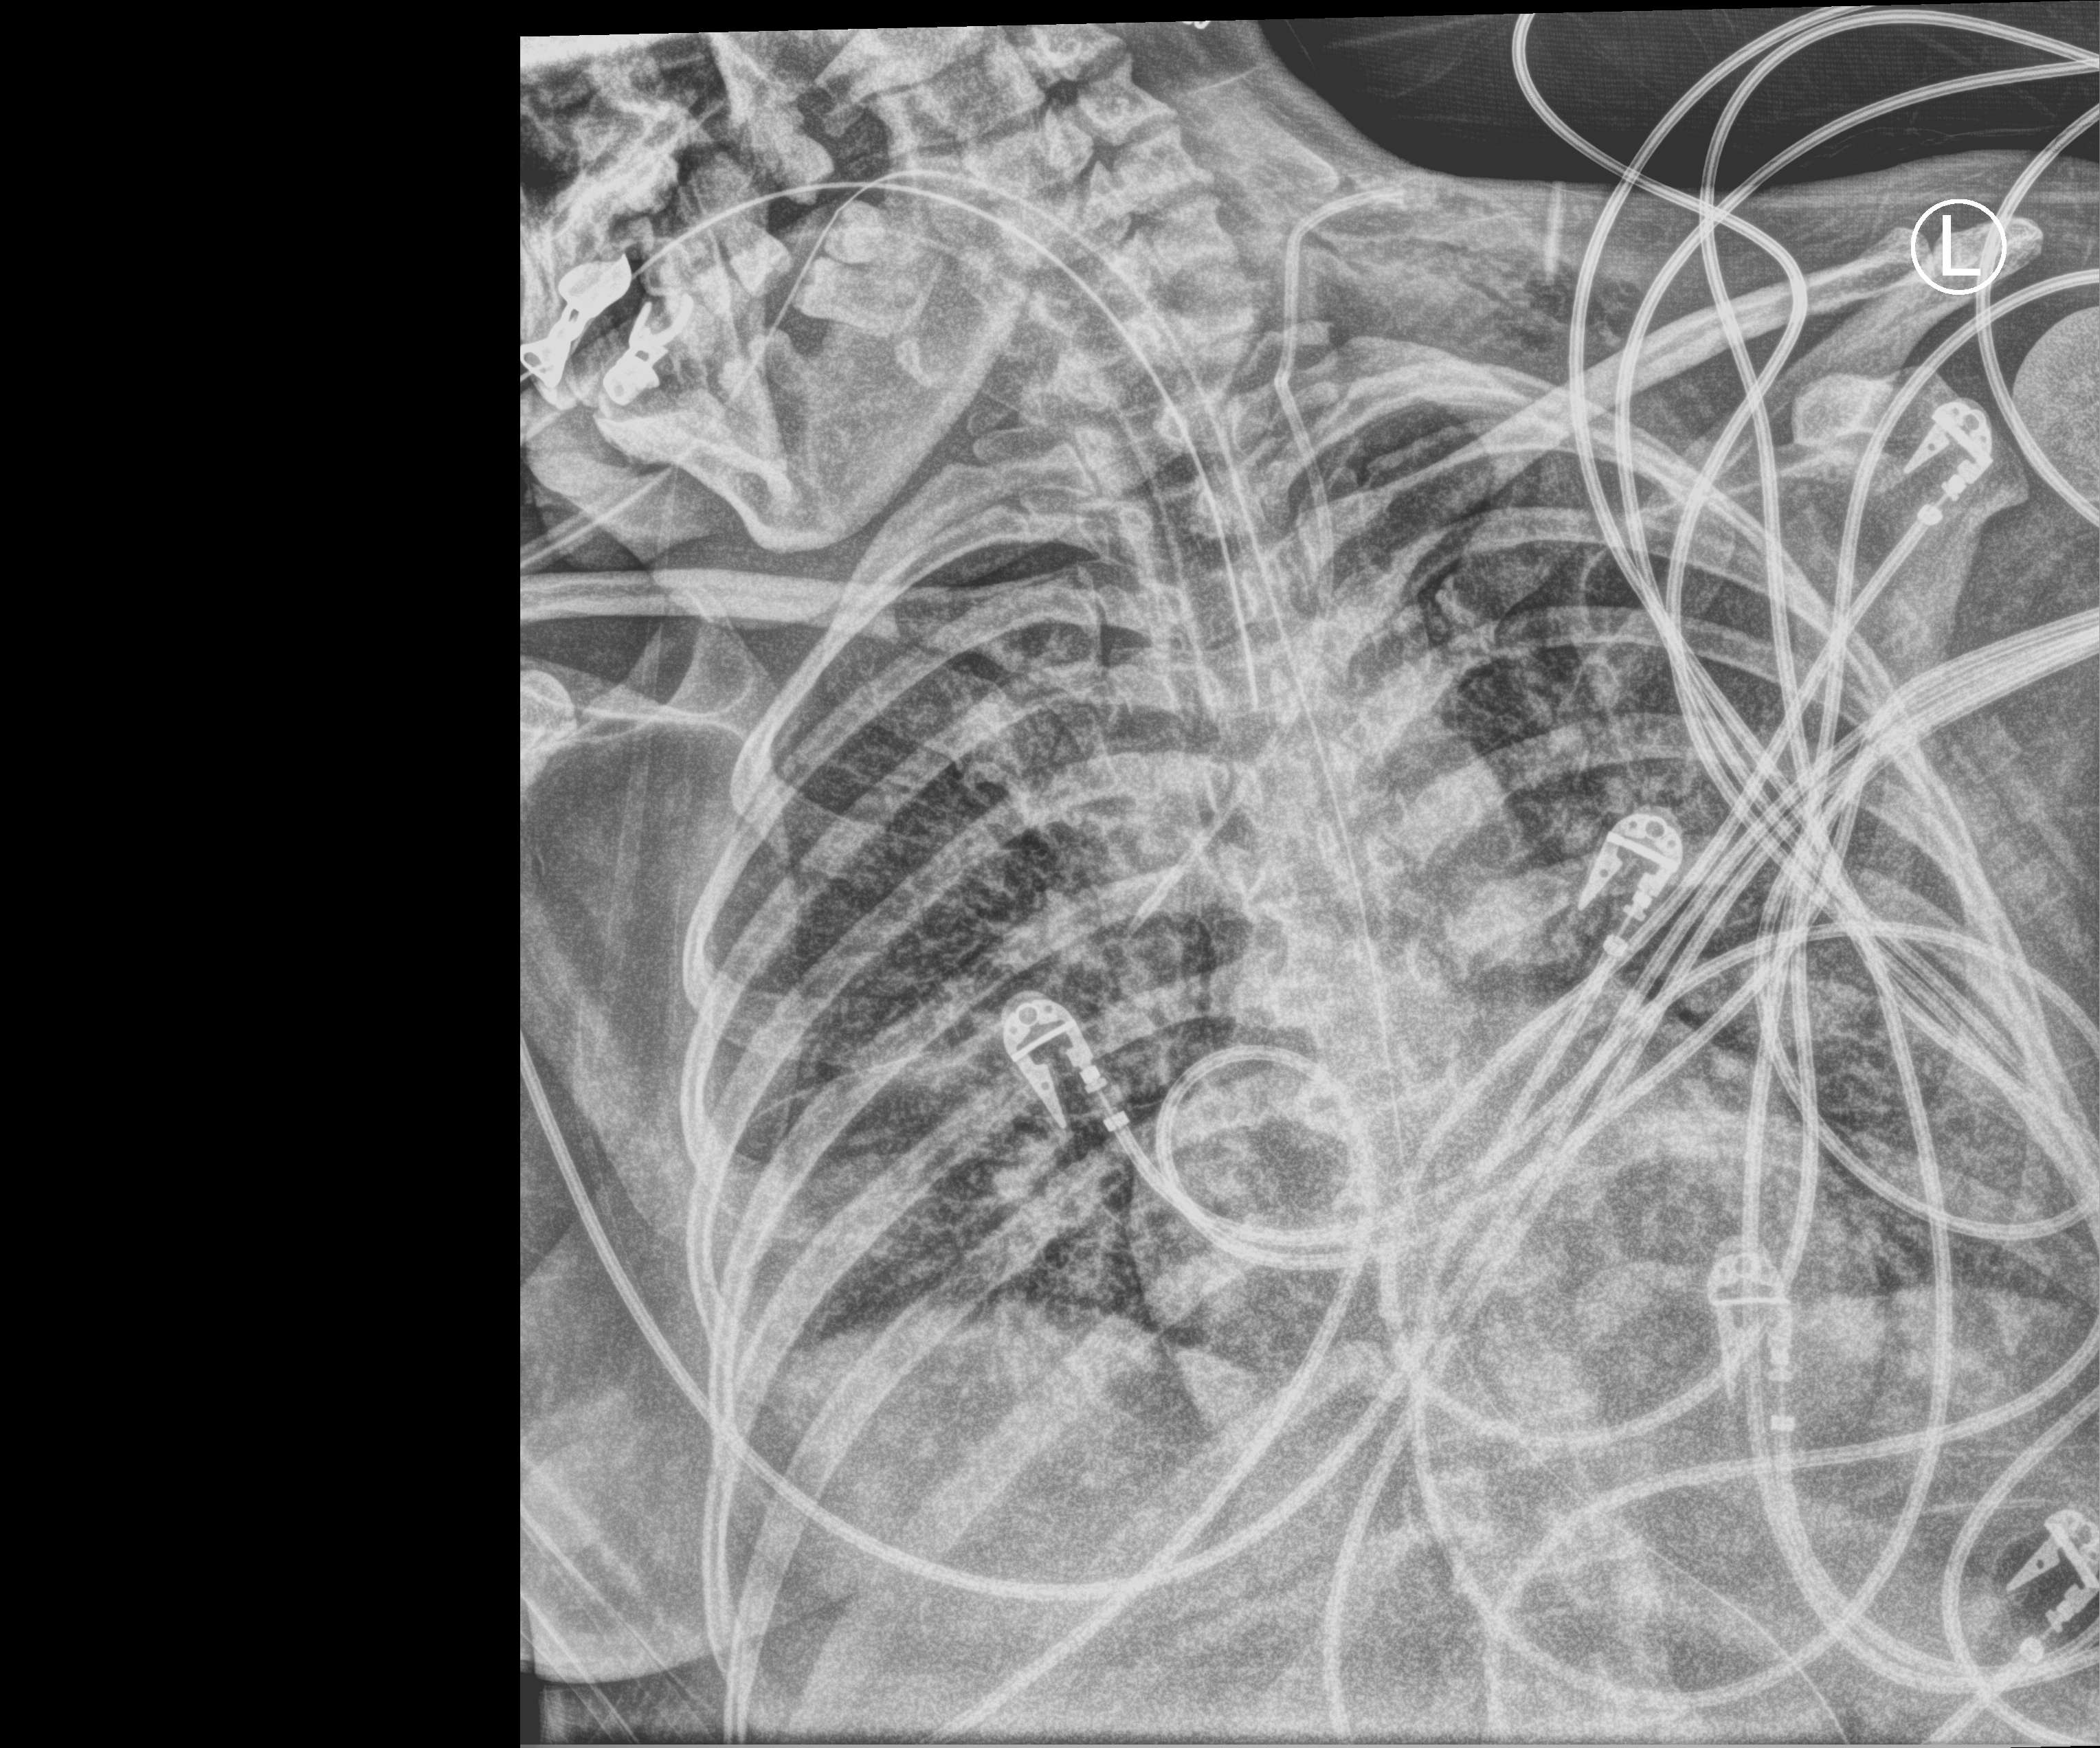
Portable chest radiograph, anteroposterior (AP) projection. Patient hospitalised with COVID-19; female, aged 18–59 years.
Admission-level facts for this patient (not findings on this image; timing relative to this image not recorded): admitted to intensive care during this hospital stay: yes; mechanically ventilated during this hospital stay: yes; length of hospital stay: 71 days.